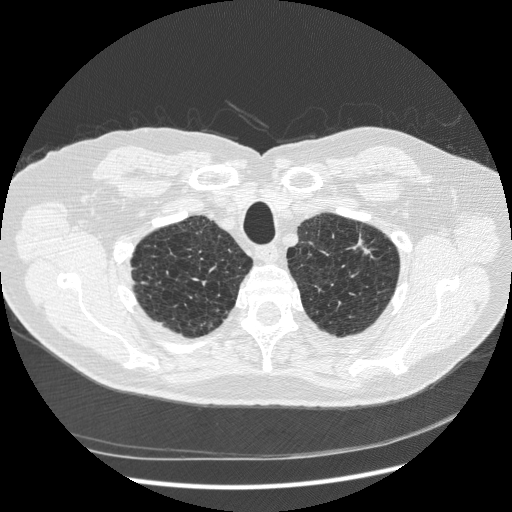
Axial slice from a low-dose chest CT screening exam; first (baseline) screen; lung window (W 1500 / L -600 HU); 1.25 mm slice thickness; standard (soft-tissue) reconstruction kernel (STANDARD); 120 kVp; 512 × 512 image matrix. Male participant, aged 70 years at enrolment. Former smoker at enrolment.
- Expert reader's lesion annotation, box from (x=332, y=220) to (x=387, y=275) px.
- The screening reader recorded 2 non-calcified nodules or masses ≥4 mm on this exam; which of them this box marks is not recorded.